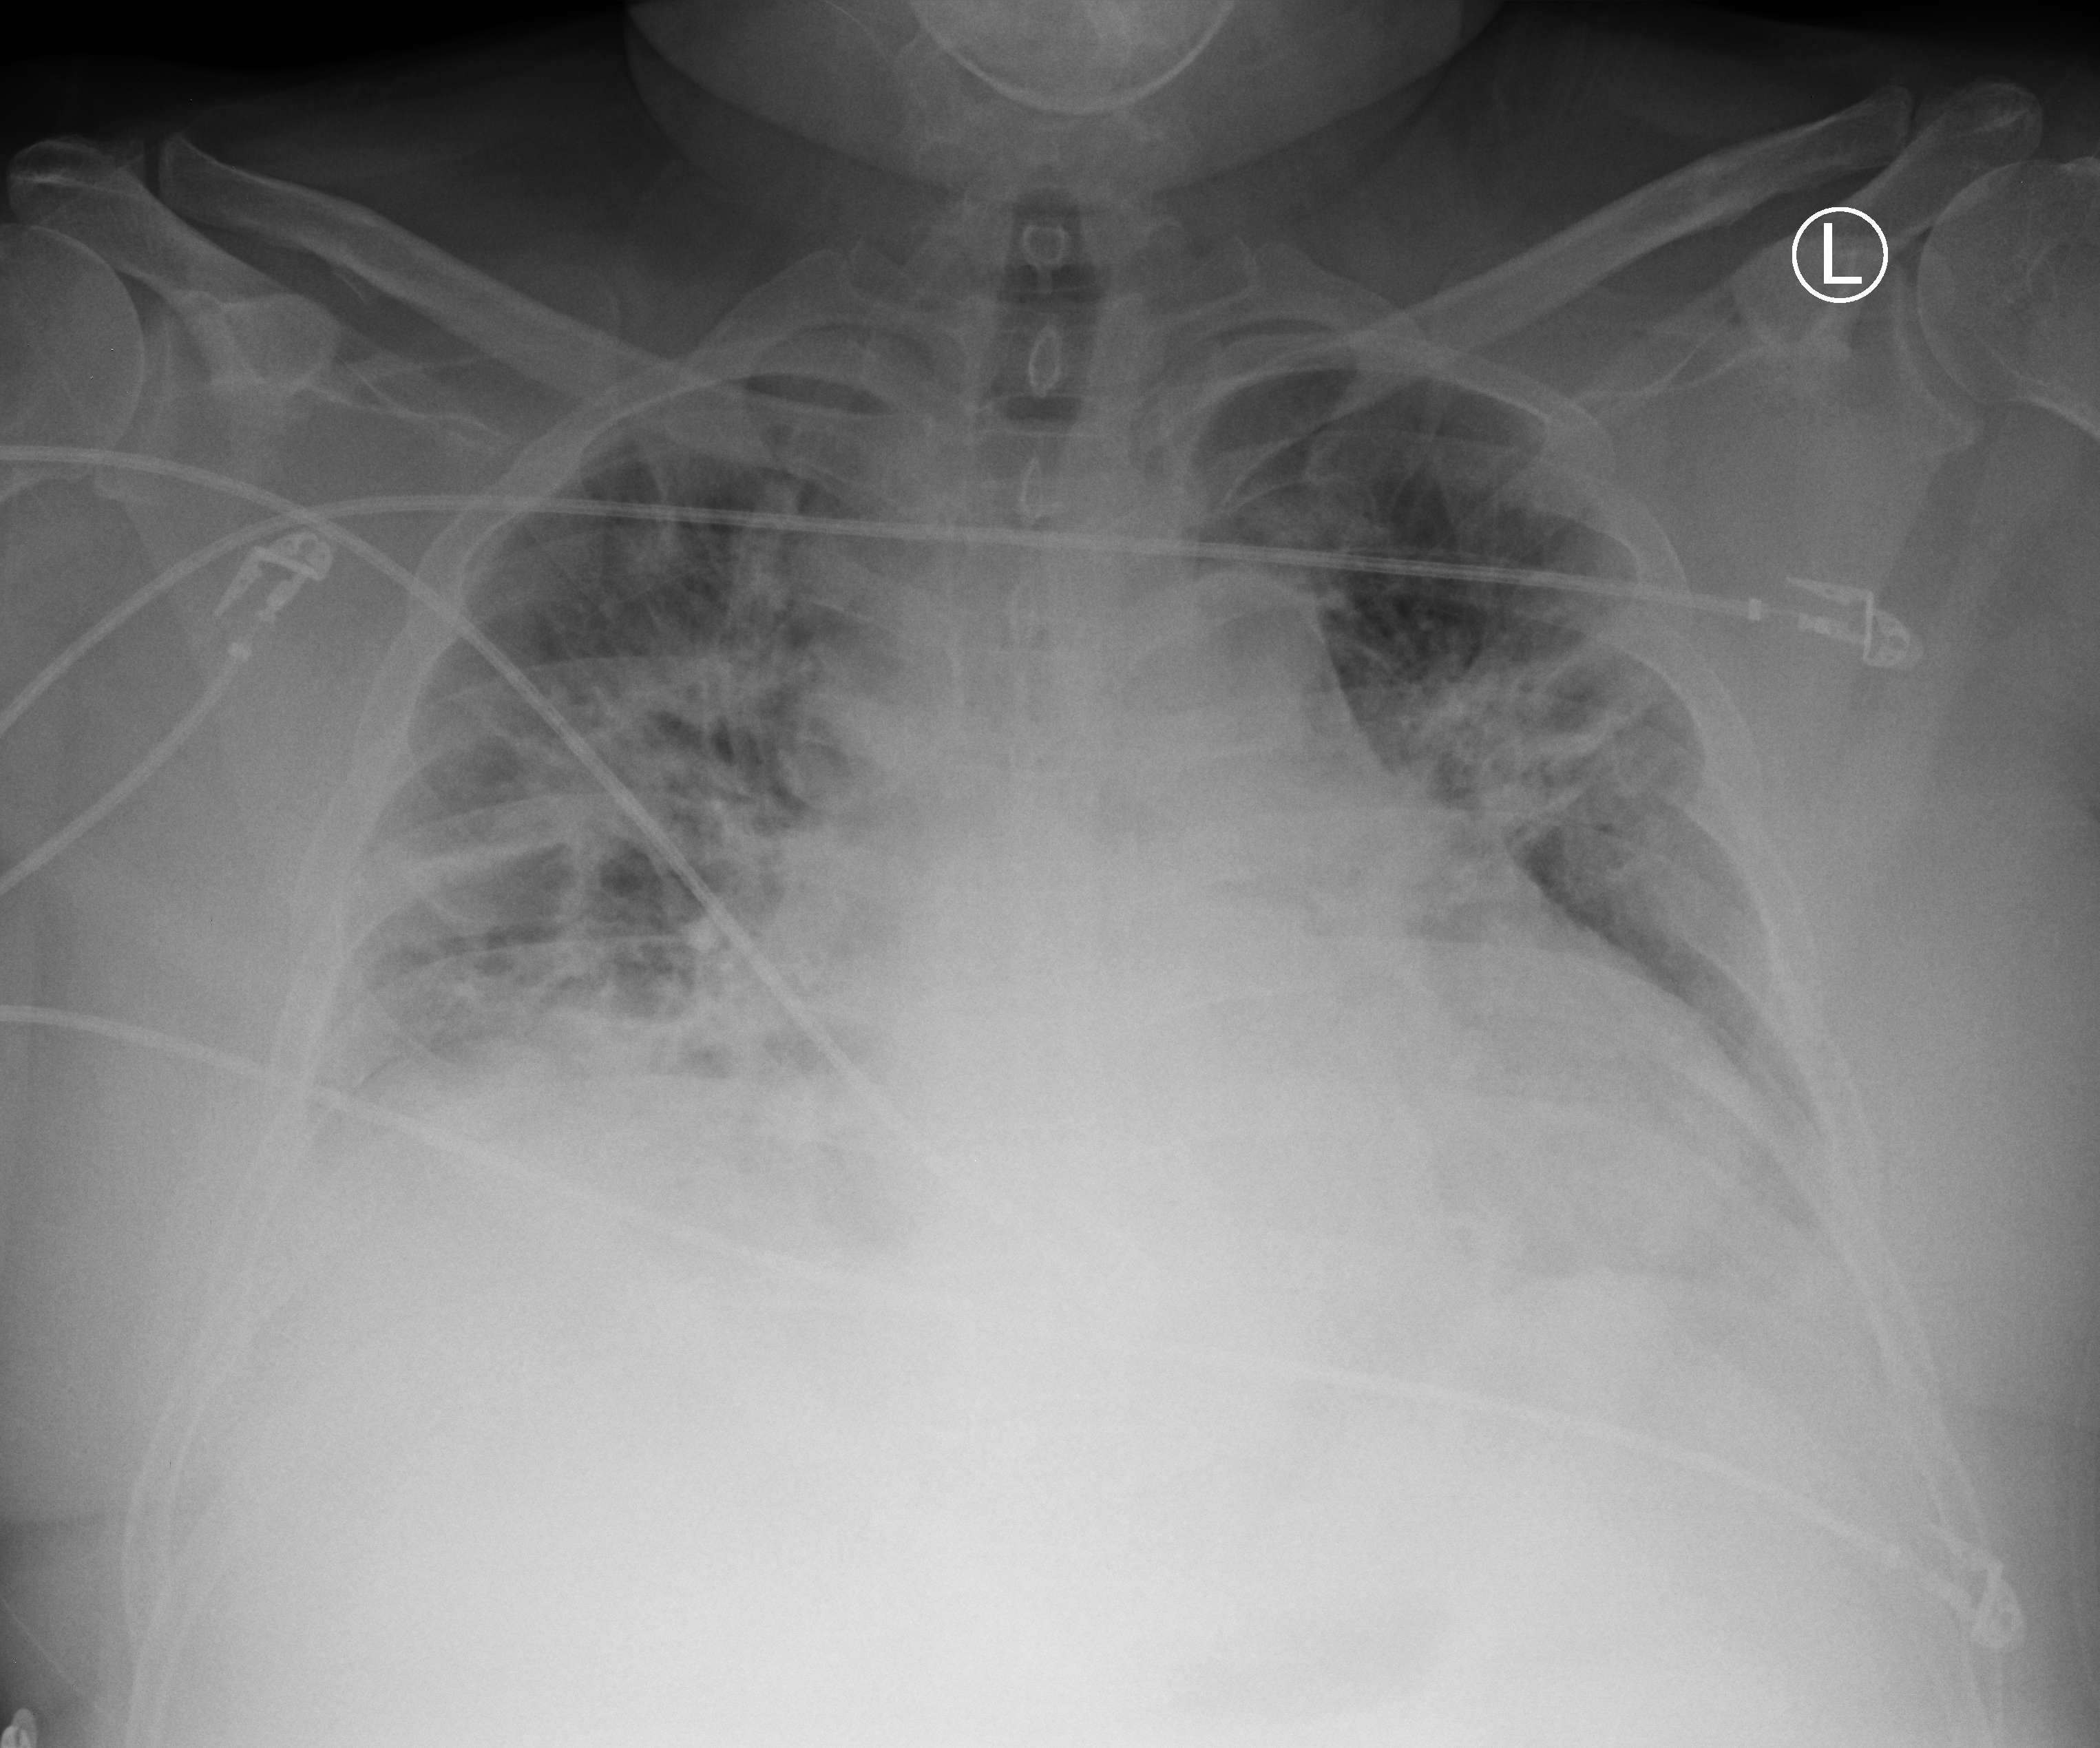
Portable chest radiograph; anteroposterior (AP) projection. Patient hospitalised with COVID-19; male, aged 18–59 years.
From the hospital-stay record, not from the radiograph (when in the stay this image was taken is not recorded): admitted to intensive care during this hospital stay: no; mechanically ventilated during this hospital stay: no.